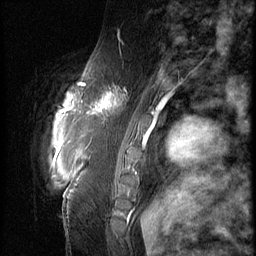
Breast MRI (dynamic contrast-enhanced), one sagittal slice. Slice 16 of 66 in the series (ordered by position). 3 images stored at this slice position (order not interpretable as contrast timing). 1.5 T. TE 4.2 ms, TR 9 ms. 2.5 mm slice thickness. 256 × 256 image matrix, field of view 180 × 180 mm. Patient: female, 57 years. From the clinical record (not read from this slice): setting: breast cancer imaged before/during neoadjuvant chemotherapy; receptor status: triple-negative.
Outlined on this slice (semi-automatic segmentation, software-assisted and operator-edited):
- analysis volume of interest (the breast-tissue region the enhancement analysis was run in; not a lesion): bounding box [x1, y1, x2, y2] px = [86, 74, 138, 129]
- tumour enhancement mask (voxels above the 140 % enhancement threshold inside the analysis volume of interest): [87, 94, 117, 117]